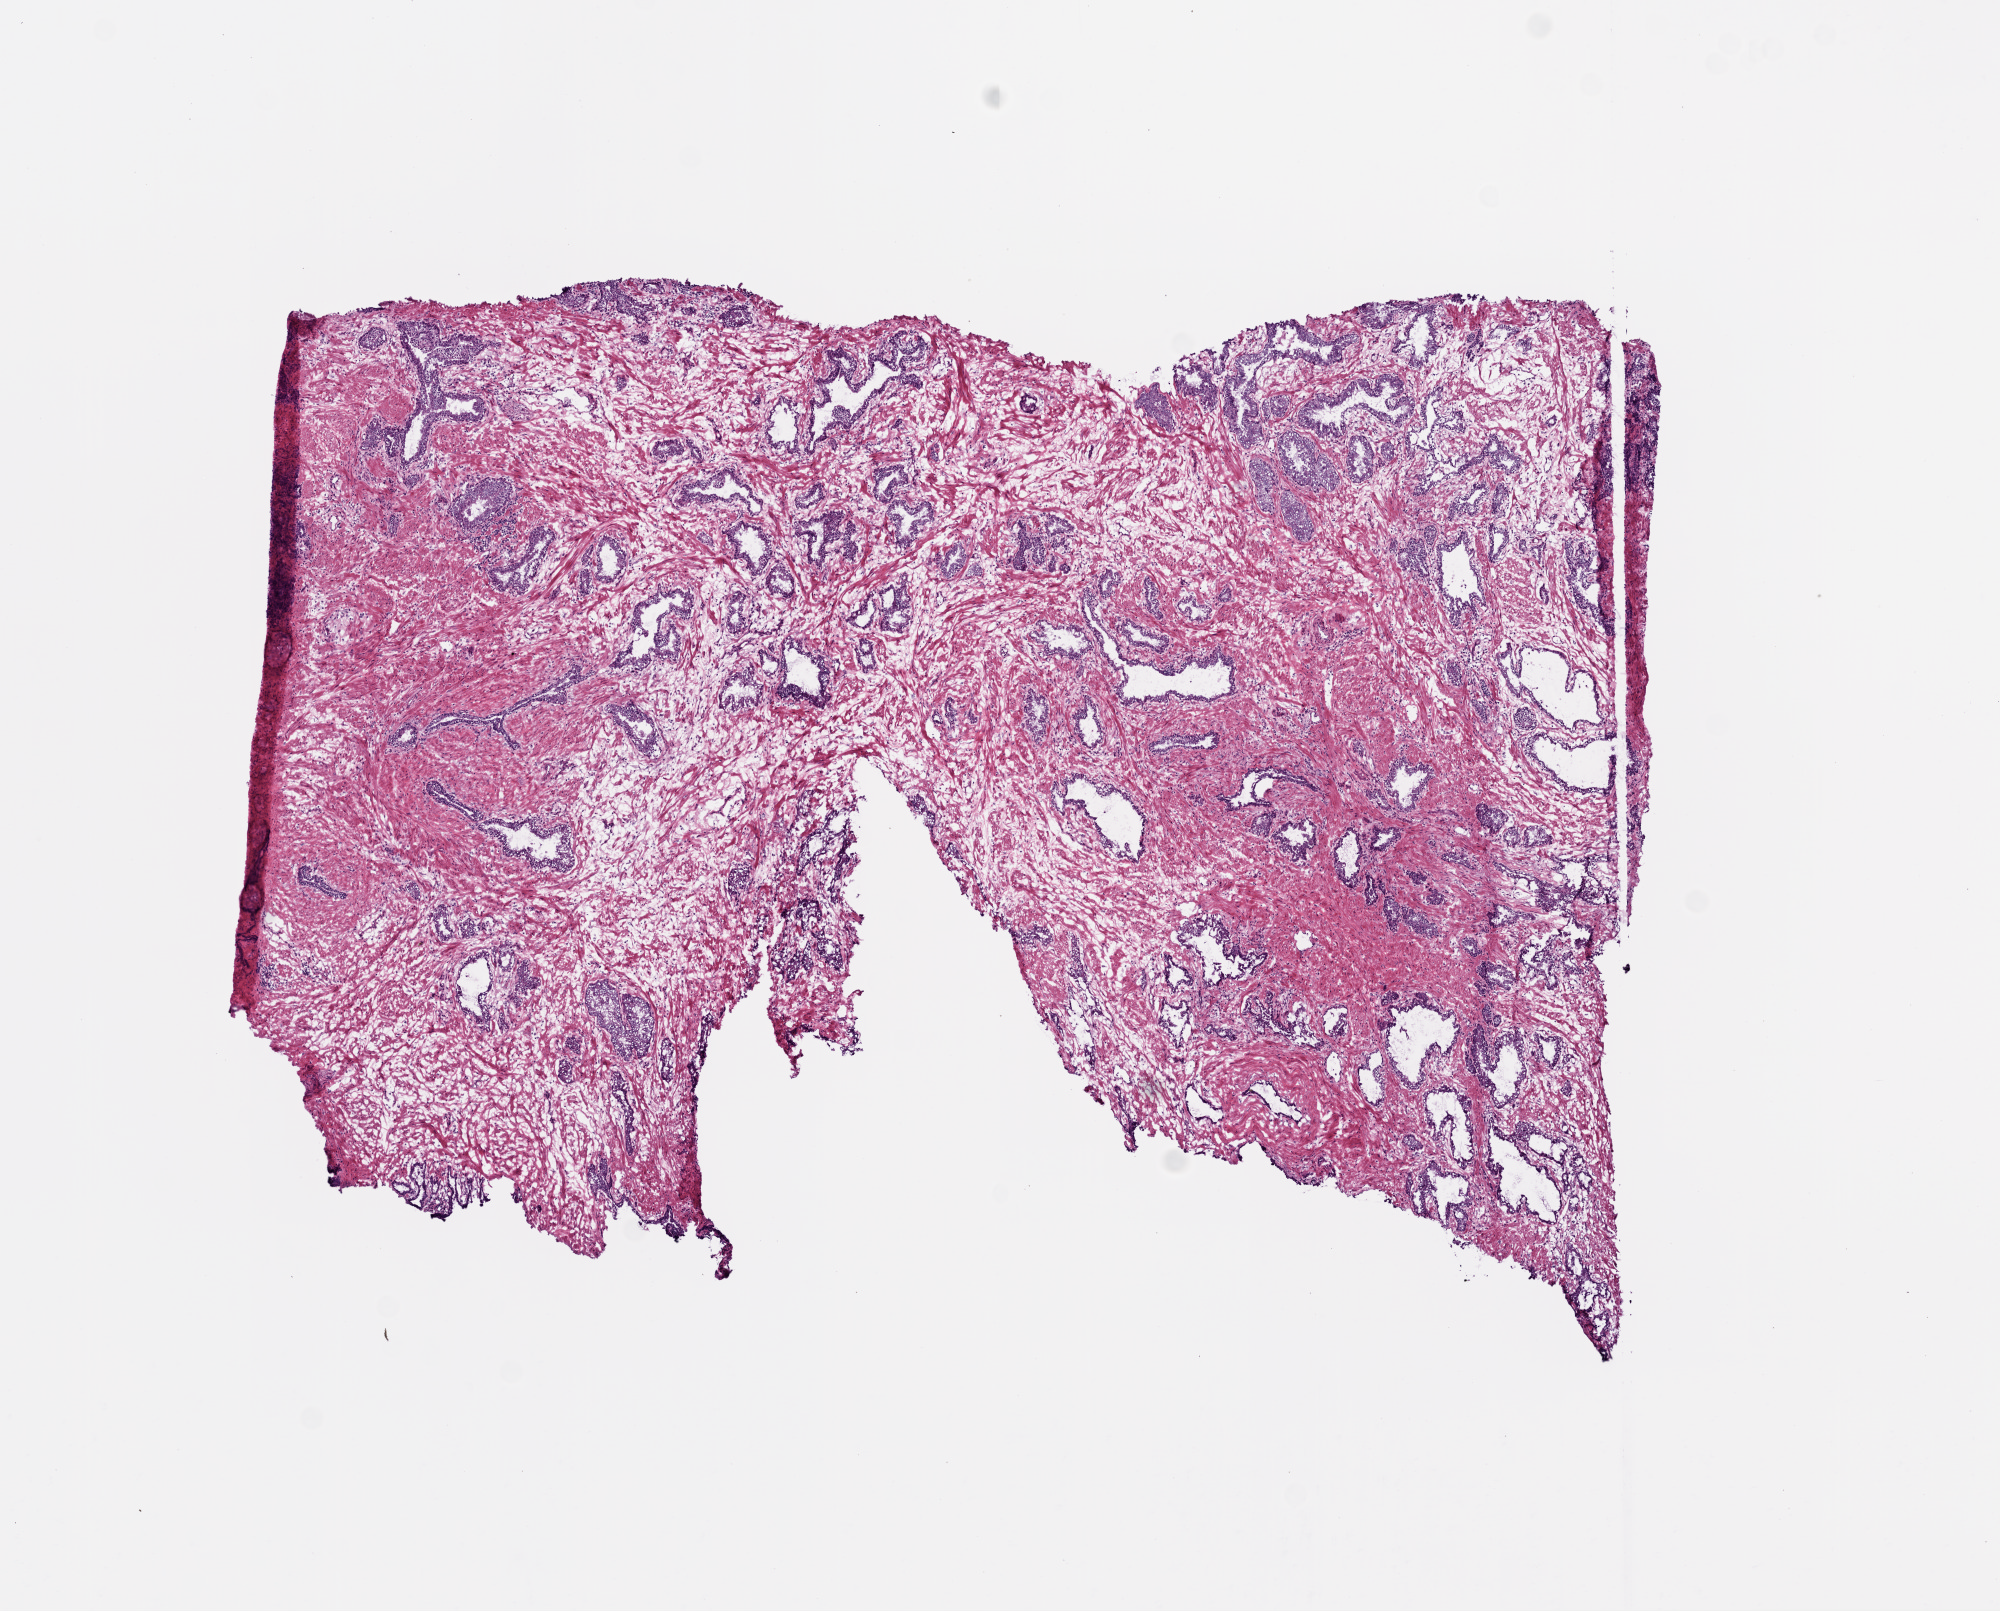
Digitized H&E tissue section (whole slide), a low-resolution overview of the entire scanned area, about 8.0 x 6.5 mm (from a 20x scan). Frozen section from the top of the tissue portion. Sample: solid tissue normal (non-tumour tissue), prostate. Male patient; age at initial diagnosis 61 years.
This section: solid tissue normal (non-tumour) sample from the same patient. Patient diagnosis: Acinar cell carcinoma (prostate gland).